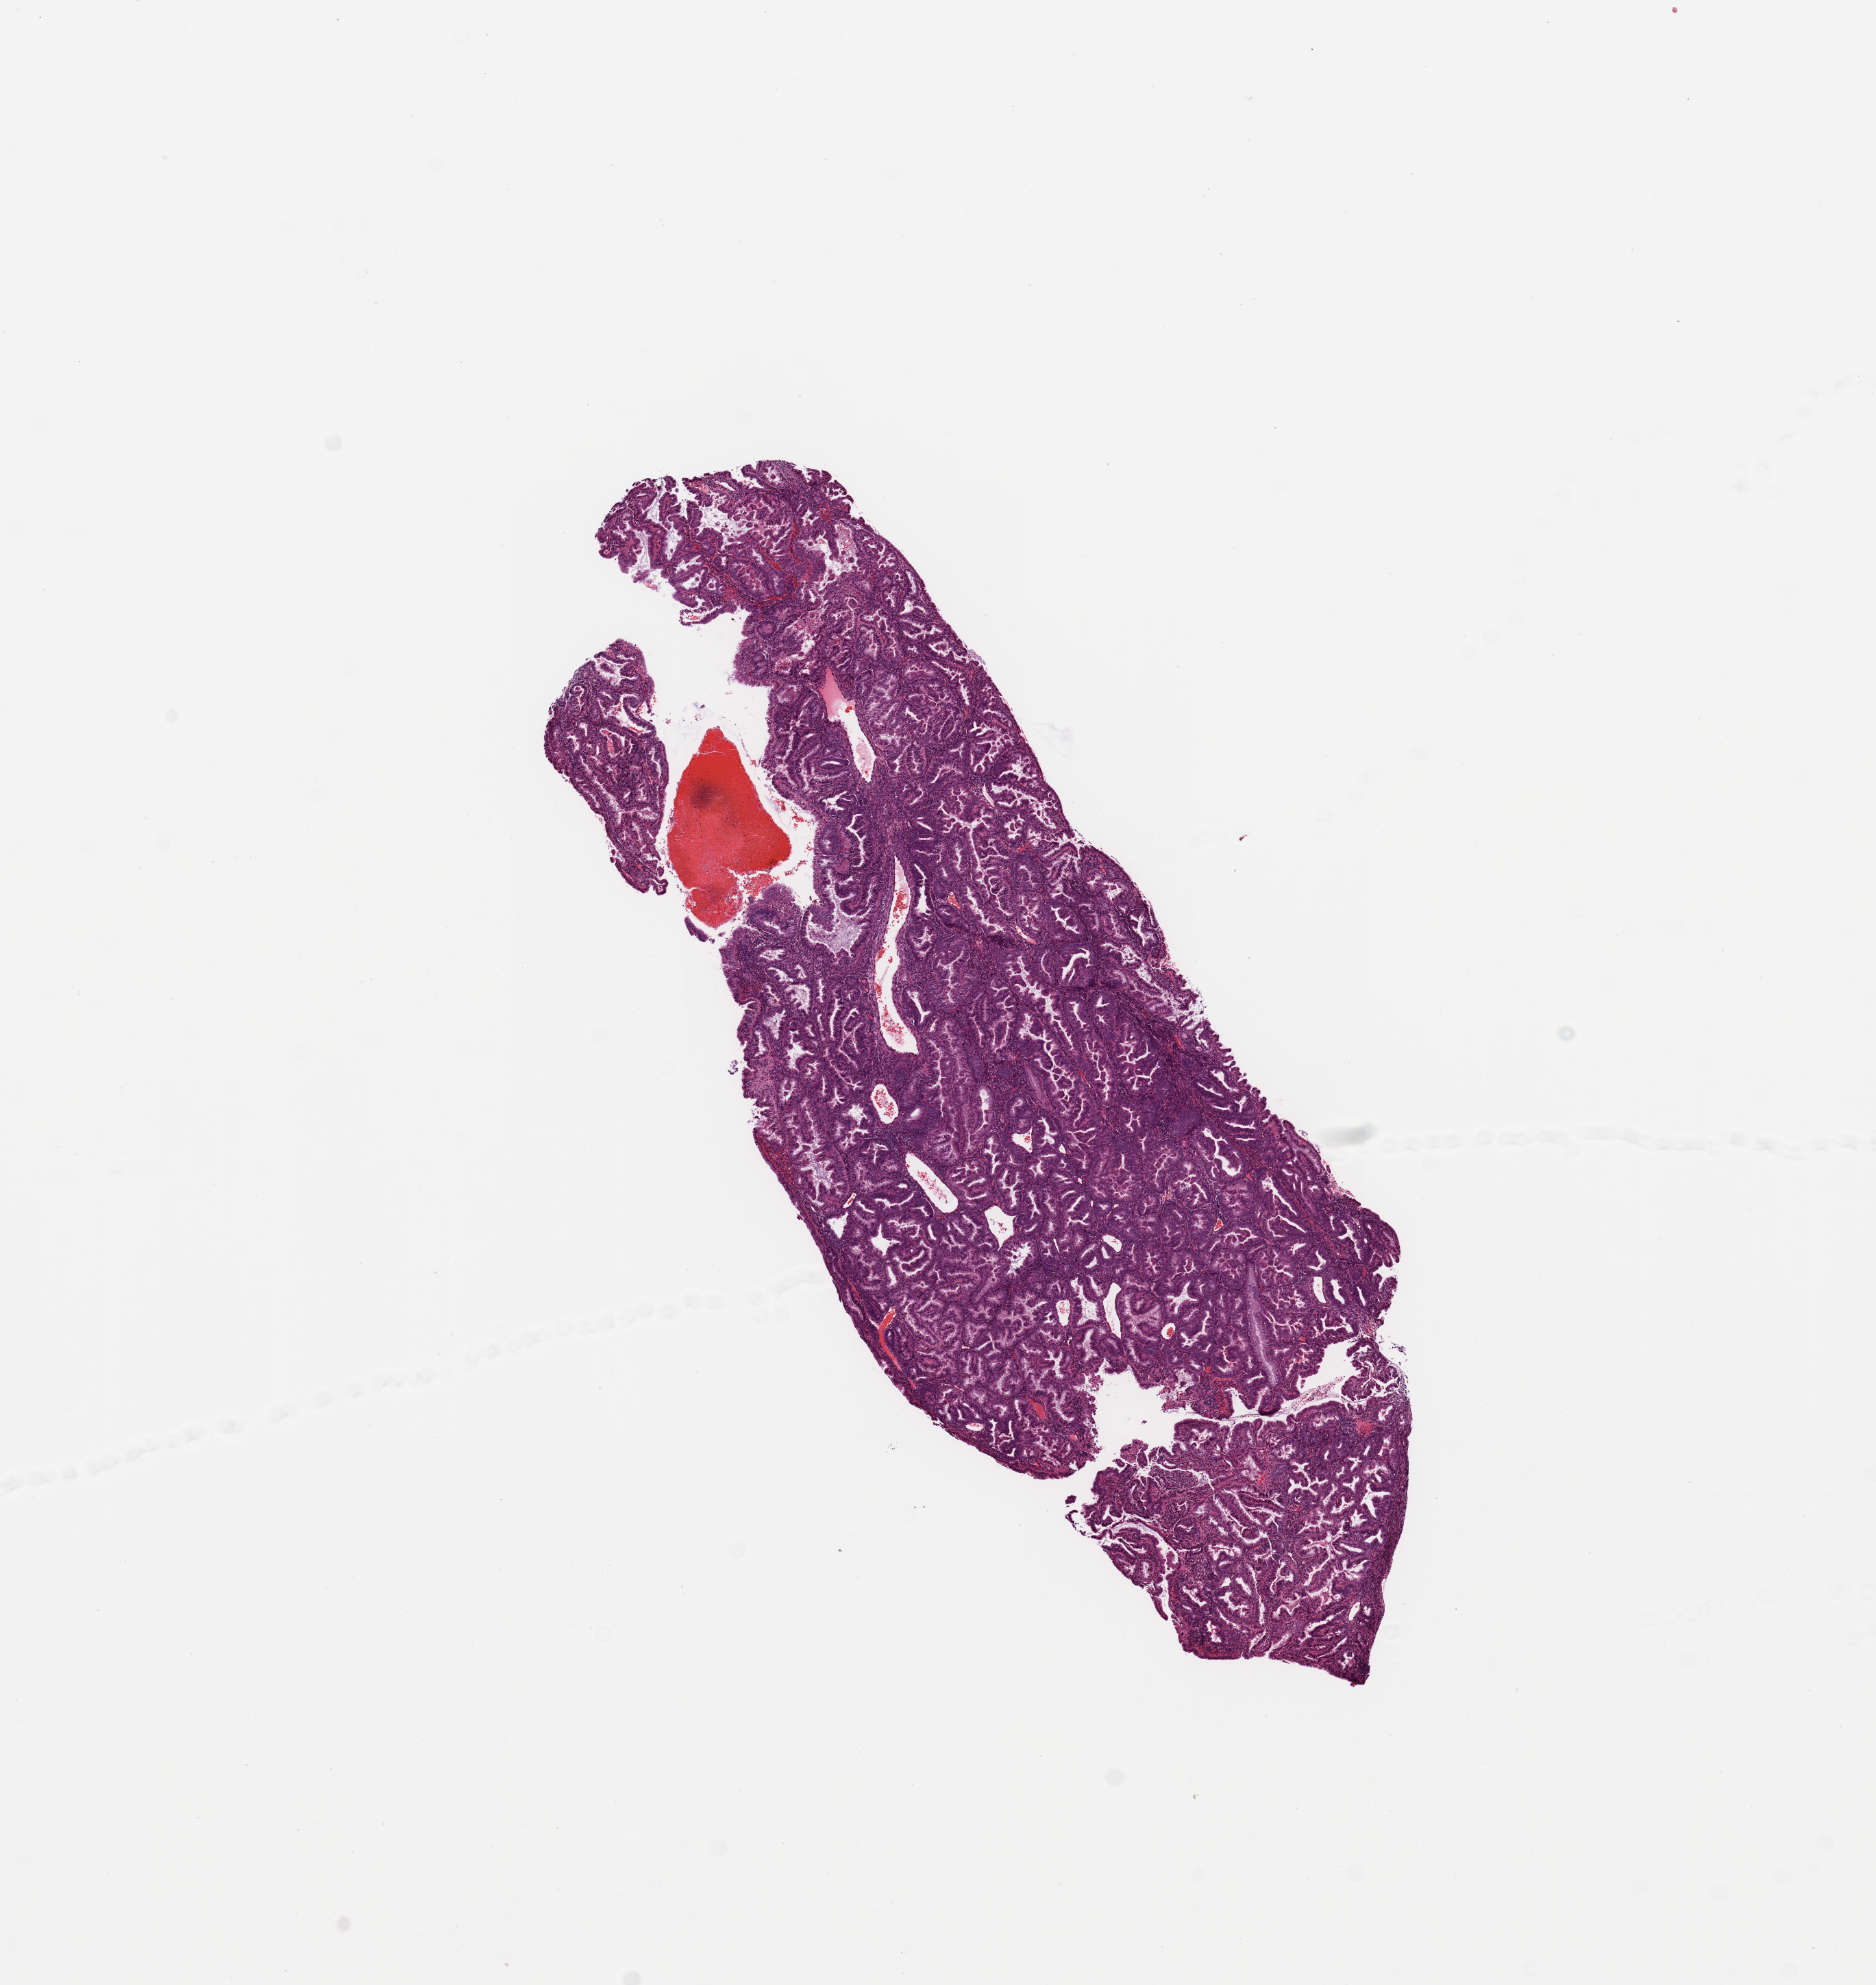
Hematoxylin and eosin (H&E) stained whole-slide image — a low-resolution overview of the entire scanned area, about 10.8 x 11.5 mm, tumour tissue sample, sampled site: uterus. Patient: female, age 60 years. Histologic grade: G1 (well differentiated). Pathologist review of this section (percent, as recorded): tumour nuclei 95%, necrosis 0%.
Diagnosis: Endometrioid adenocarcinoma, NOS. AJCC pathologic stage: I.